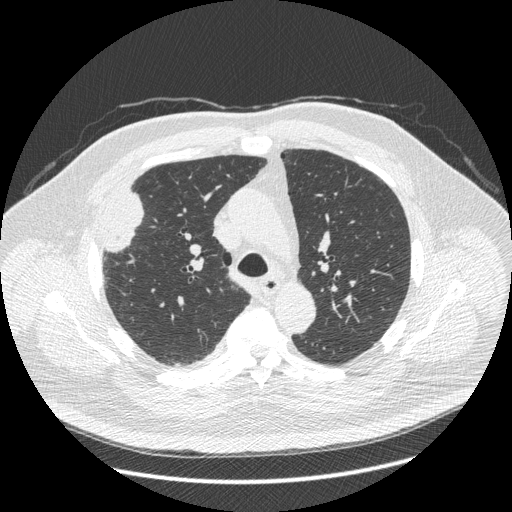
Chest CT (low-dose screening protocol), one axial image, third screening round (two years after baseline), lung window (W 1500 / L -600 HU), standard (soft-tissue) reconstruction kernel (STANDARD), slice 132 of 426 in the series. Male, age 66 years at enrolment. Current smoker at enrolment.
Lesion marked by an expert reader, bounding box [x1, y1, x2, y2] px = [87, 196, 146, 268]. Screening reader's record for this exam (one nodule recorded; not confirmed to be the boxed lesion): non-calcified nodule or mass ≥4 mm, right upper lobe, 48 × 25 mm, spiculated (stellate) margins, soft tissue attenuation, pre-existing on the prior screen: no. Official screen result: positive, other. Later outcome: lung cancer diagnosed 35 days after this screen — non-small cell carcinoma, right upper lobe, stage IV (AJCC 6th edition), 50 mm at pathology.